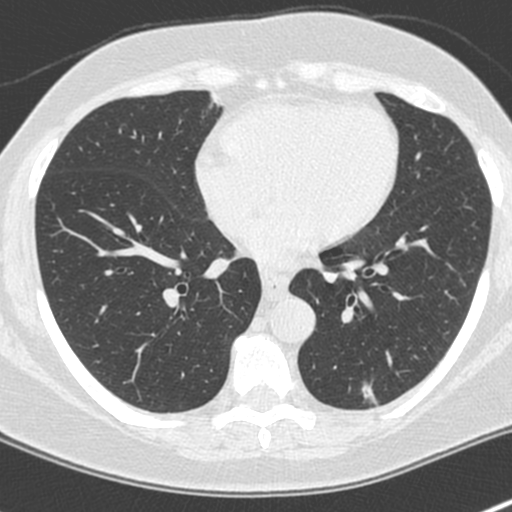
Axial slice from a low-dose chest CT screening exam, baseline annual screen, lung window (W 1500 / L -600 HU). Female, age 64 years at enrolment. Former smoker at enrolment.
- Expert reader's lesion annotation, bounding box <346,371,391,418> (left, top, right, bottom; pixels).
- No non-calcified nodule or mass ≥4 mm was recorded by the screening reader at this exam.
- Participant outcome: lung cancer diagnosed 549 days after this screen — adenocarcinoma, NOS, left lower lobe, poorly differentiated (G3), stage IA (AJCC 6th edition), 8 mm at pathology.